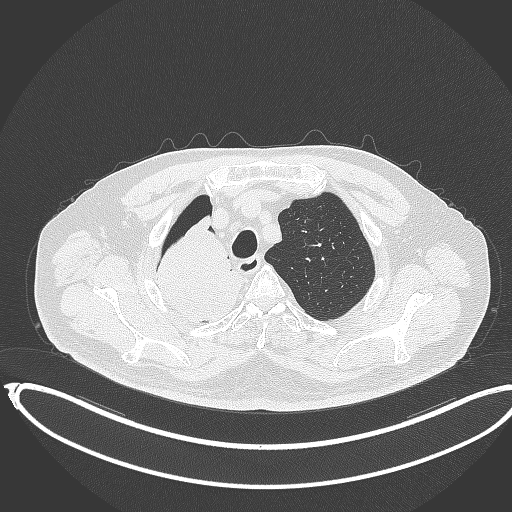
Chest CT, one axial slice. Slice 307 of 403 in the series (ordered by position). 120 kVp. Lung window (W 1500 / L -600 HU). 1 mm slice thickness. 512 × 512 image matrix, field of view 436 × 436 mm. Patient: male, 68 years. Case-level facts recorded for this patient, not image findings: clinical TNM (as recorded): T2a N0 M0.
Annotated regions visible in this slice (bounding box drawn by a radiologist):
- lung tumour (recorded histology: adenocarcinoma): bounding box [x1, y1, x2, y2] px = [145, 220, 254, 326]